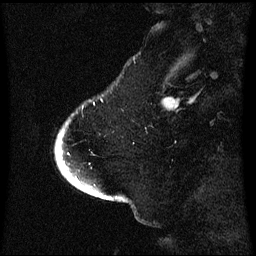
Breast MRI (dynamic contrast-enhanced), one sagittal slice; position 11 of 60 along the scan axis; dynamic contrast-enhanced series, image 2 of 3 at this slice position (ordered by acquisition); 1.5 T; TE 4.2 ms, TR 8.4 ms; 2.1 mm slice thickness; 256 × 256 image matrix. Female patient, age 53 years. Case-level facts recorded for this patient, not image findings: setting: breast cancer imaged before/during neoadjuvant chemotherapy; receptor status: HR-positive, HER2-negative.
Outlined on this slice (semi-automatically segmented with operator editing):
- analysis volume of interest (the breast-tissue region the enhancement analysis was run in; not a lesion): bounding box <56,124,71,171> (left, top, right, bottom; pixels)
- tumour enhancement mask (voxels above the 70 % enhancement threshold inside the analysis volume of interest): <59,158,67,171>